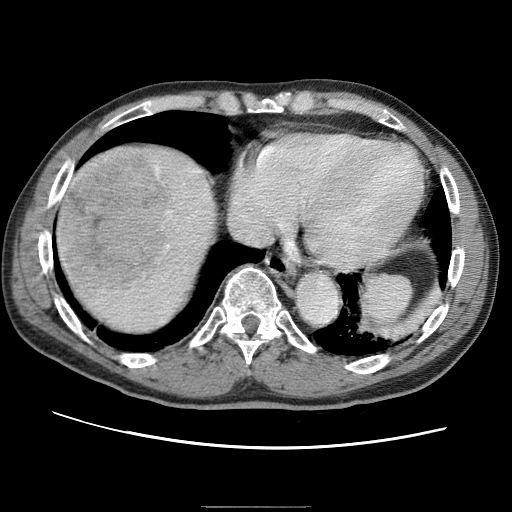
Contrast-enhanced abdominal CT (liver protocol), one axial slice. Position 61 of 75 along the scan axis. Reconstruction kernel STANDARD. 120 kVp. One of 2 acquisitions stored at this slice position. Soft-tissue window (W 400 / L 40 HU). 512 × 512 image matrix. Case-level facts recorded for this patient, not image findings: diagnosis: hepatocellular carcinoma (patient treated with transarterial chemoembolisation; whether this scan precedes or follows treatment is not stated here); TNM stage (as recorded): Stage-II; Child-Pugh class: A; tumour differentiation: well differentiated.
Structures marked on this image (semi-automatically segmented with operator editing):
- liver parenchyma outside the tumour (the mass and vessels are separate outlines, so this box may not span the whole liver): bounding box <56,144,220,336> (left, top, right, bottom; pixels)
- mass: <59,147,179,297>
- liver vessels: <58,147,179,228>